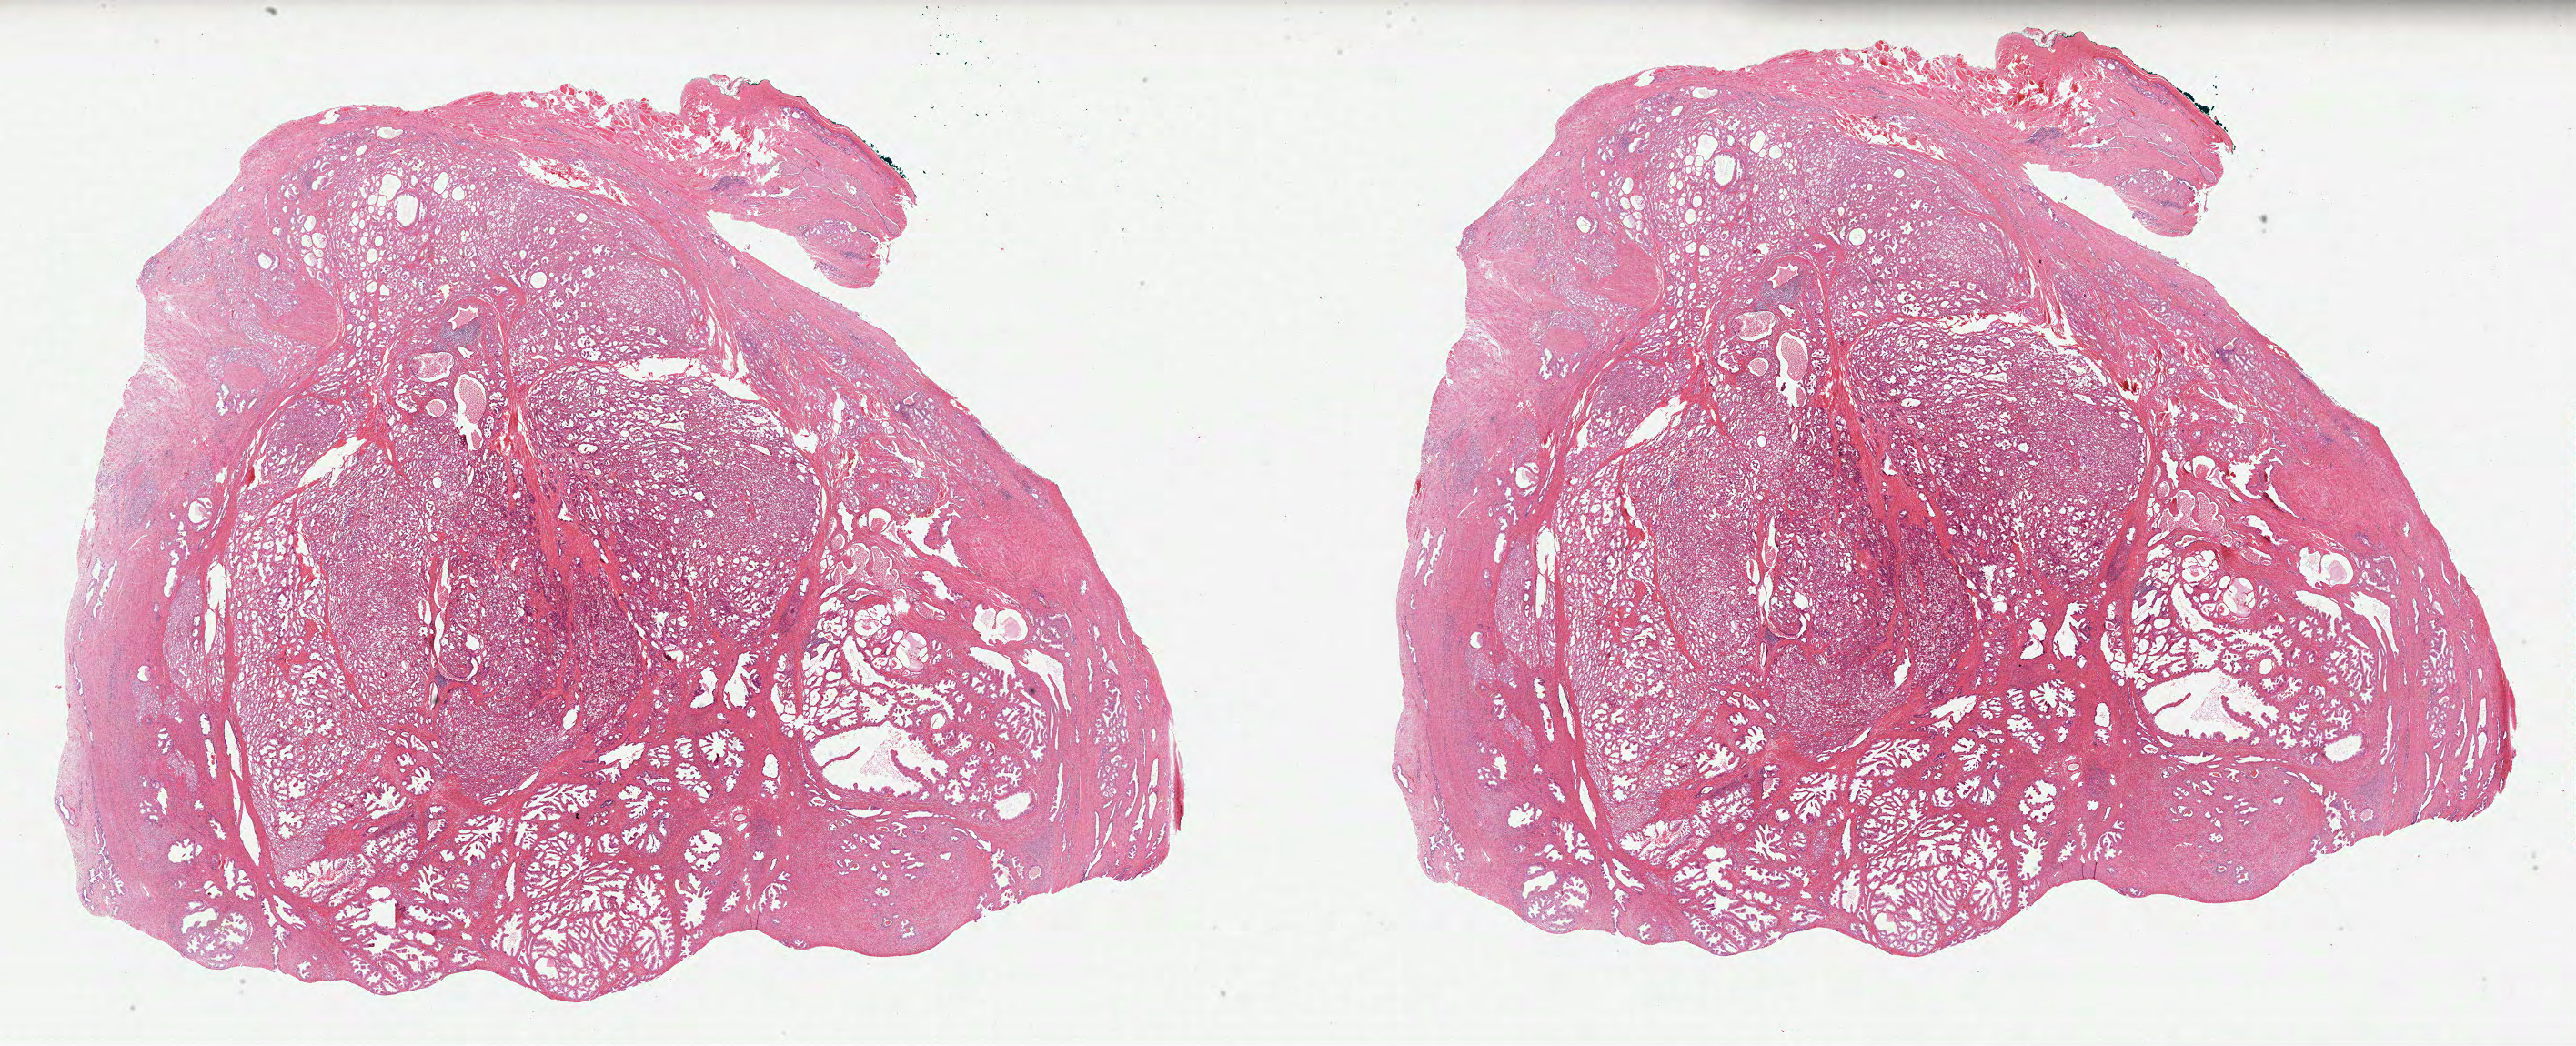
Hematoxylin and eosin (H&E) stained whole-slide image, shown as a low-resolution overview of the whole scanned area (about 45.7 x 18.6 mm, acquisition: 40x scan). FFPE section. Prostate, primary tumour sample. Patient: male, age at initial diagnosis 54 years. Gleason score: 7 (3+4).
Pathologic diagnosis: Acinar cell carcinoma. Laterality: bilateral.